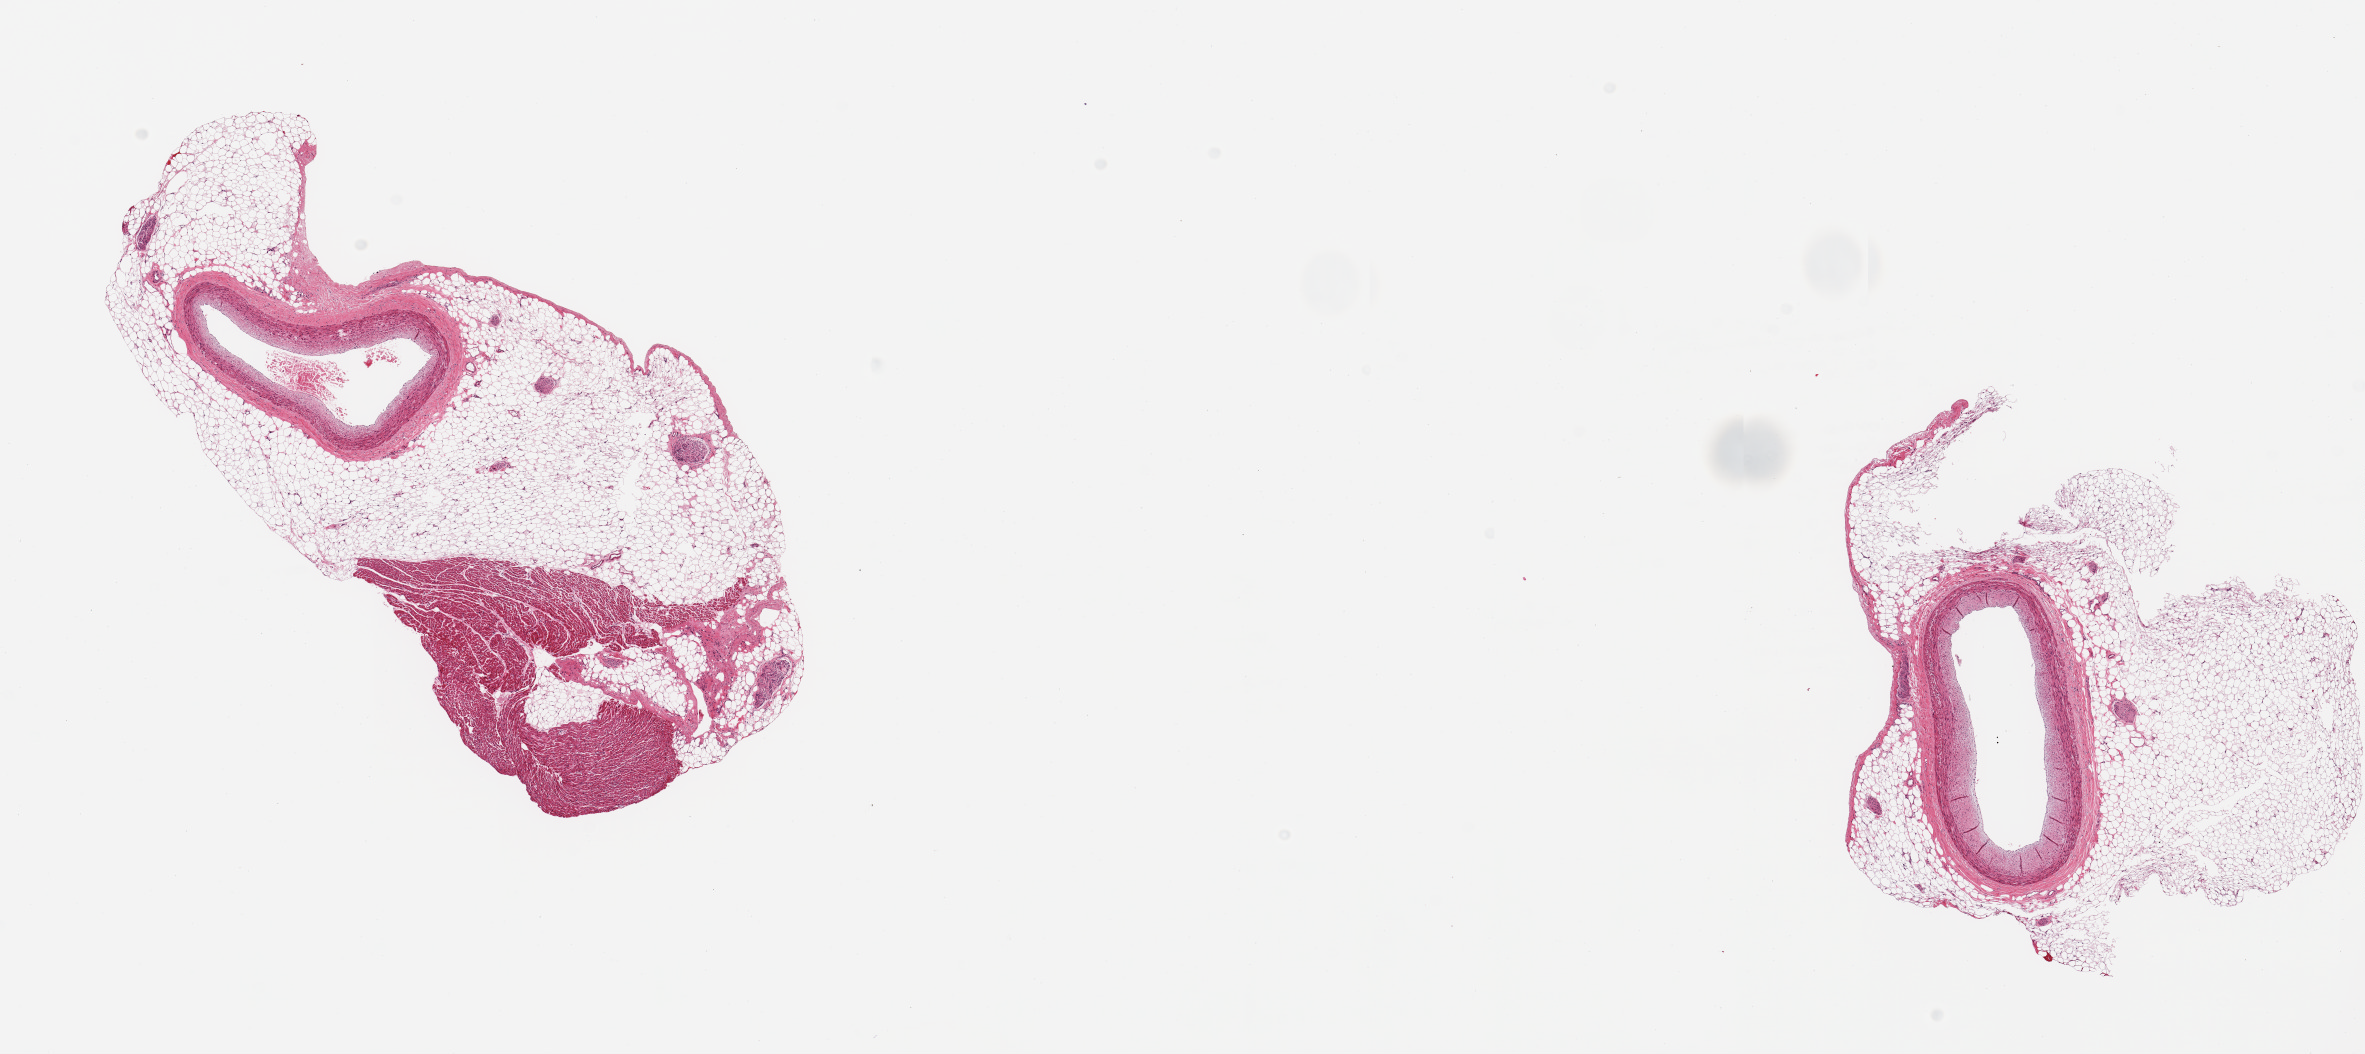
Haematoxylin and eosin whole-slide image, brightfield, a low-resolution overview of the entire scanned area, about 18.7 x 8.3 mm (slide scanned at 20x); PAXgene-fixed paraffin-embedded (PFPE) section; sampled site (target tissue): coronary artery; tissue donor sample. Donor sex: male.
Reviewer comment on this tissue sample: 2 pieces, correct target but abundant adherent fat/myocardium are ~80% of specimen.